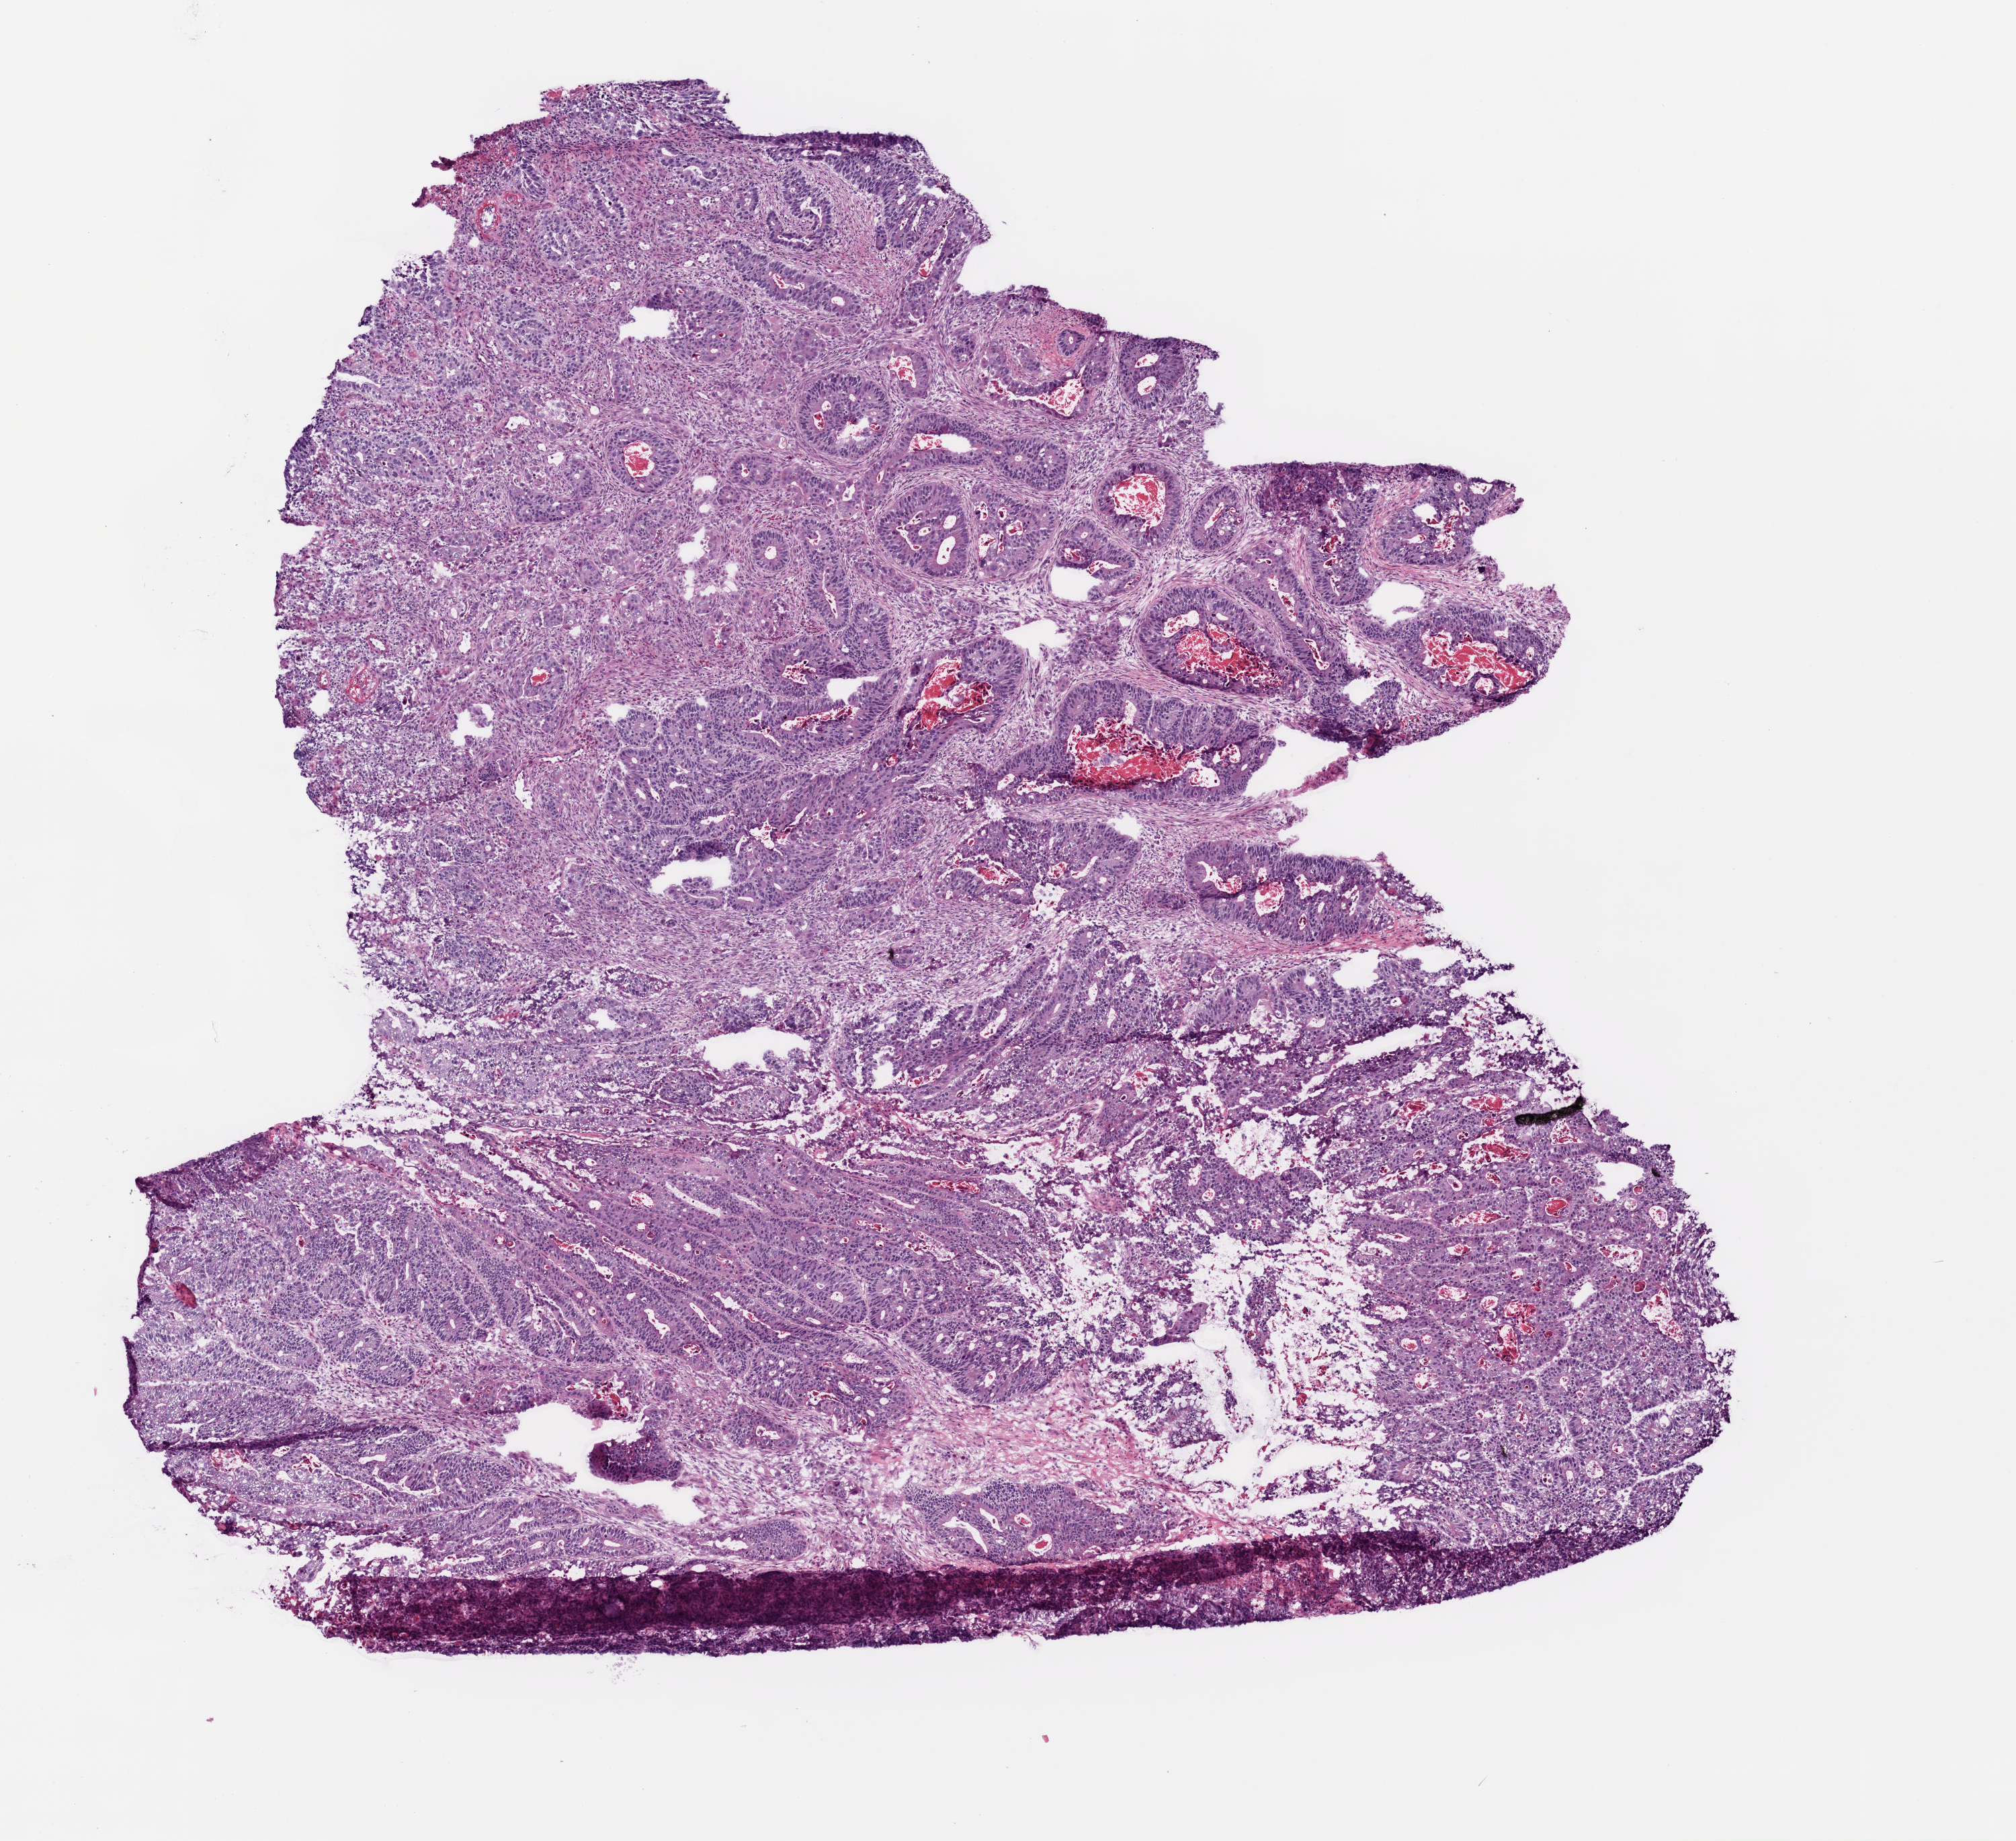
Whole-slide histology image, Hematoxylin and eosin (H&E) stained — a low-resolution overview of the entire scanned area, about 6.0 x 5.5 mm, frozen section from the top of the tissue portion, colon, primary tumour sample. Patient: male, age at initial diagnosis 77 years. Composition of this section per pathologist review: tumour cells 95%, tumour nuclei 80%, normal cells 0%, stromal cells 0%, necrosis 5%.
Lymph nodes positive (case pathology): 2 of 33 examined. AJCC pathologic stage: IIIB (6th edition). Diagnosis: Adenocarcinoma, NOS.